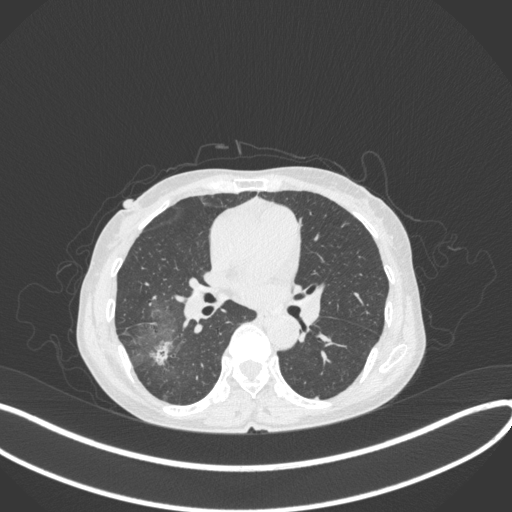
Chest CT, one axial slice. Position 209 of 379 along the scan axis. Reconstruction kernel B31f. Lung window (W 1500 / L -600 HU). 512 × 512 image matrix. Patient: female, 69 years. Case-level facts recorded for this patient, not image findings: clinical TNM (as recorded): T1b N0 M0; histopathological grade: G2-3.
Annotated regions visible in this slice (rectangle marked by the reading radiologist):
- lung tumour (recorded histology: adenocarcinoma): bounding box <146,335,176,367> (left, top, right, bottom; pixels)